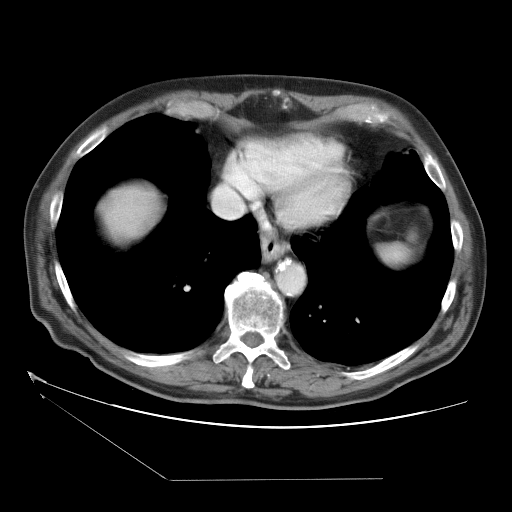
Contrast-enhanced abdominal CT (liver protocol), one axial slice. Slice 34 of 38 in the series (ordered by position). Reconstruction kernel STANDARD. One of 2 acquisitions stored at this slice position. Soft-tissue window (W 400 / L 40 HU). 5 mm slice thickness. 512 × 512 image matrix. Case-level facts recorded for this patient, not image findings: diagnosis: hepatocellular carcinoma (patient treated with transarterial chemoembolisation; whether this scan precedes or follows treatment is not stated here); TNM stage (as recorded): Stage-II; Child-Pugh class: A; tumour differentiation: moderately differentiated; tumour size: 0.8 cm.
Outlined on this slice (semi-automatic segmentation, software-assisted and operator-edited):
- liver parenchyma outside the tumour (the mass and vessels are separate outlines, so this box may not span the whole liver): box from (x=104, y=188) to (x=158, y=237) px